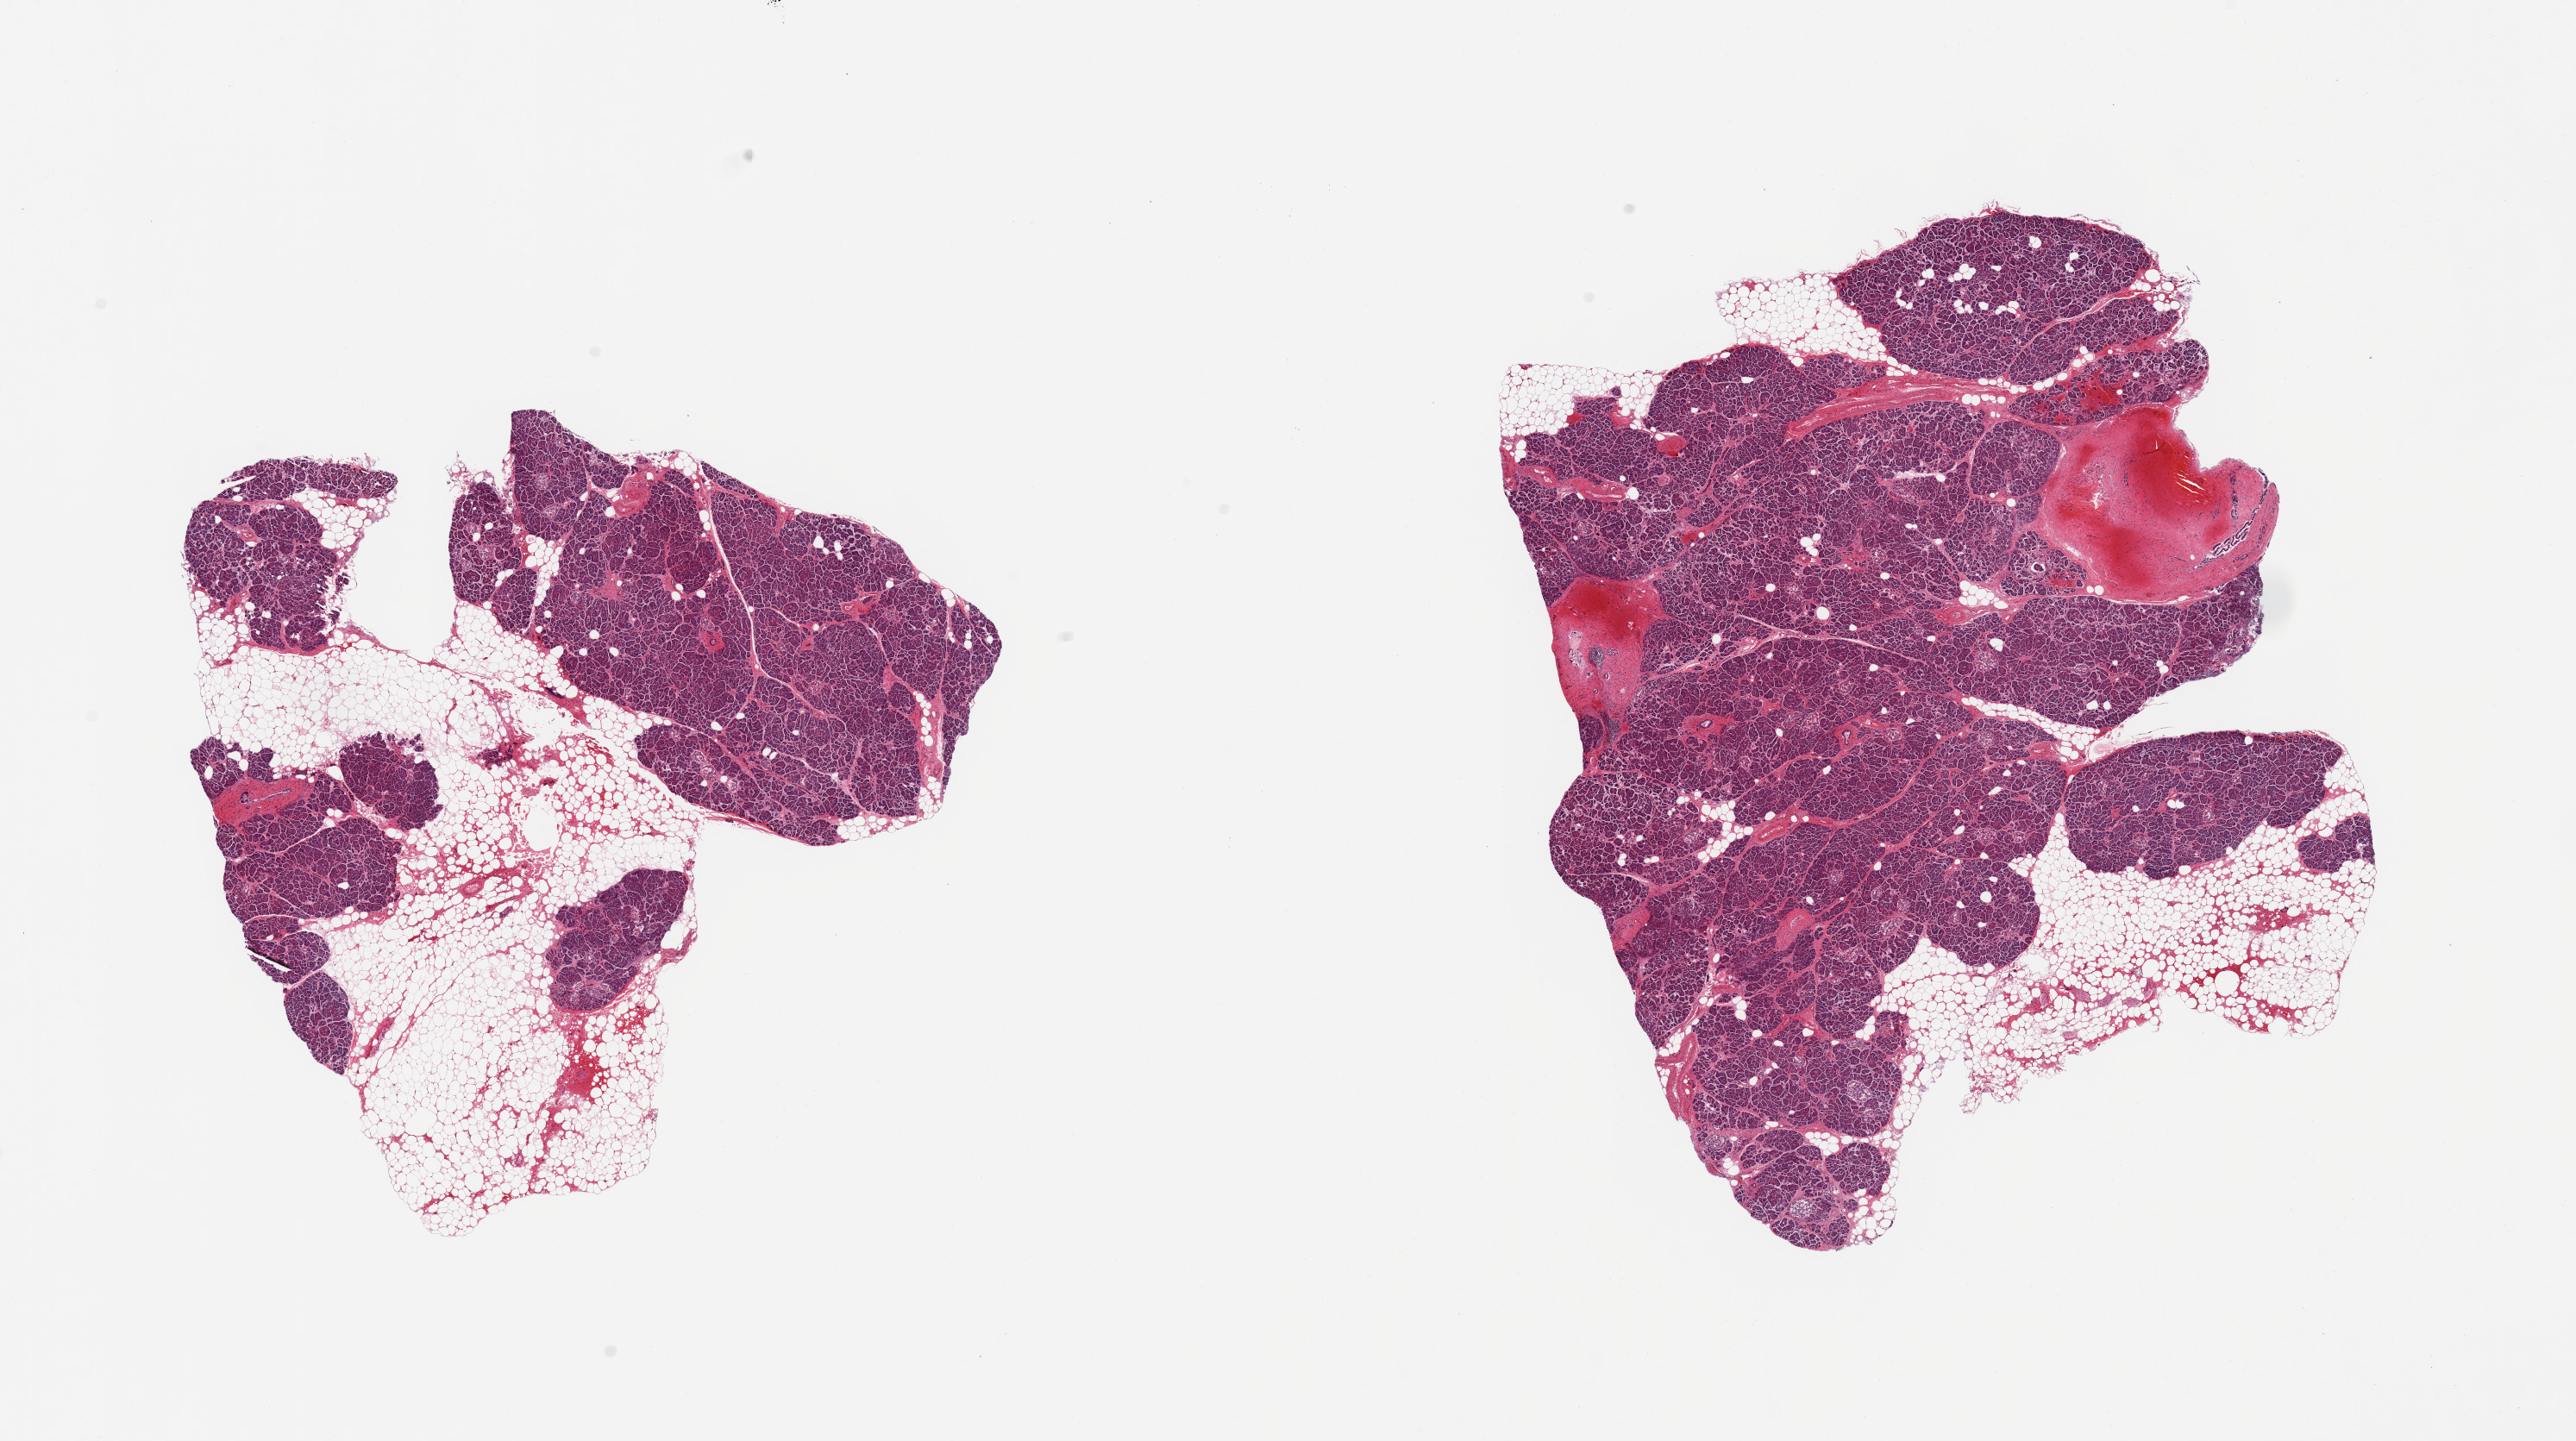
Haematoxylin and eosin whole-slide image, a low-resolution overview of the entire scanned area, about 23.6 x 13.2 mm; PAXgene-fixed paraffin-embedded (PFPE) section; sampled site (target tissue): pancreas; tissue donor sample. Donor sex: male.
- review note (as recorded): 2 pieces, ~30% interstitial/adherent fat, delineatd, Islets fairly well preserved